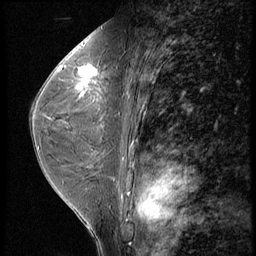
Breast MRI (dynamic contrast-enhanced), one sagittal slice. Position 31 of 56 along the scan axis. 3 images stored at this slice position (order not interpretable as contrast timing). 1.5 T. TE 4.2 ms, TR 9 ms. 256 × 256 image matrix, field of view 180 × 180 mm. Female patient, age 44 years. From the clinical record (not read from this slice): setting: breast cancer imaged before/during neoadjuvant chemotherapy; receptor status: triple-negative.
Structures marked on this image (semi-automatically segmented with operator editing):
- analysis volume of interest (the breast-tissue region the enhancement analysis was run in; not a lesion): bounding box [x1, y1, x2, y2] px = [71, 54, 112, 99]
- tumour enhancement mask (voxels above the 140 % enhancement threshold inside the analysis volume of interest): [75, 66, 101, 89]